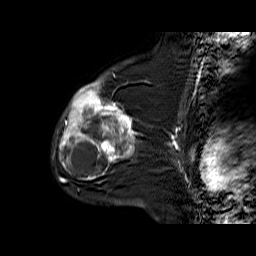
Breast MRI (dynamic contrast-enhanced), one sagittal slice; dynamic contrast-enhanced series, time point 2 of 6 at this slice position (early post-contrast); 1.5 T; TE 6.3 ms, TR 32.9 ms; 256 × 256 image matrix, field of view 200 × 200 mm. Female patient. From the clinical record (not read from this slice): setting: breast cancer imaged before/during neoadjuvant chemotherapy; receptor status: triple-negative.
Outlined on this slice (semi-automatic segmentation, software-assisted and operator-edited):
- analysis volume of interest (the breast-tissue region the enhancement analysis was run in; not a lesion): bounding box <56,76,138,170> (left, top, right, bottom; pixels)
- tumour enhancement mask (voxels above the 100 % enhancement threshold inside the analysis volume of interest): <59,80,135,162>